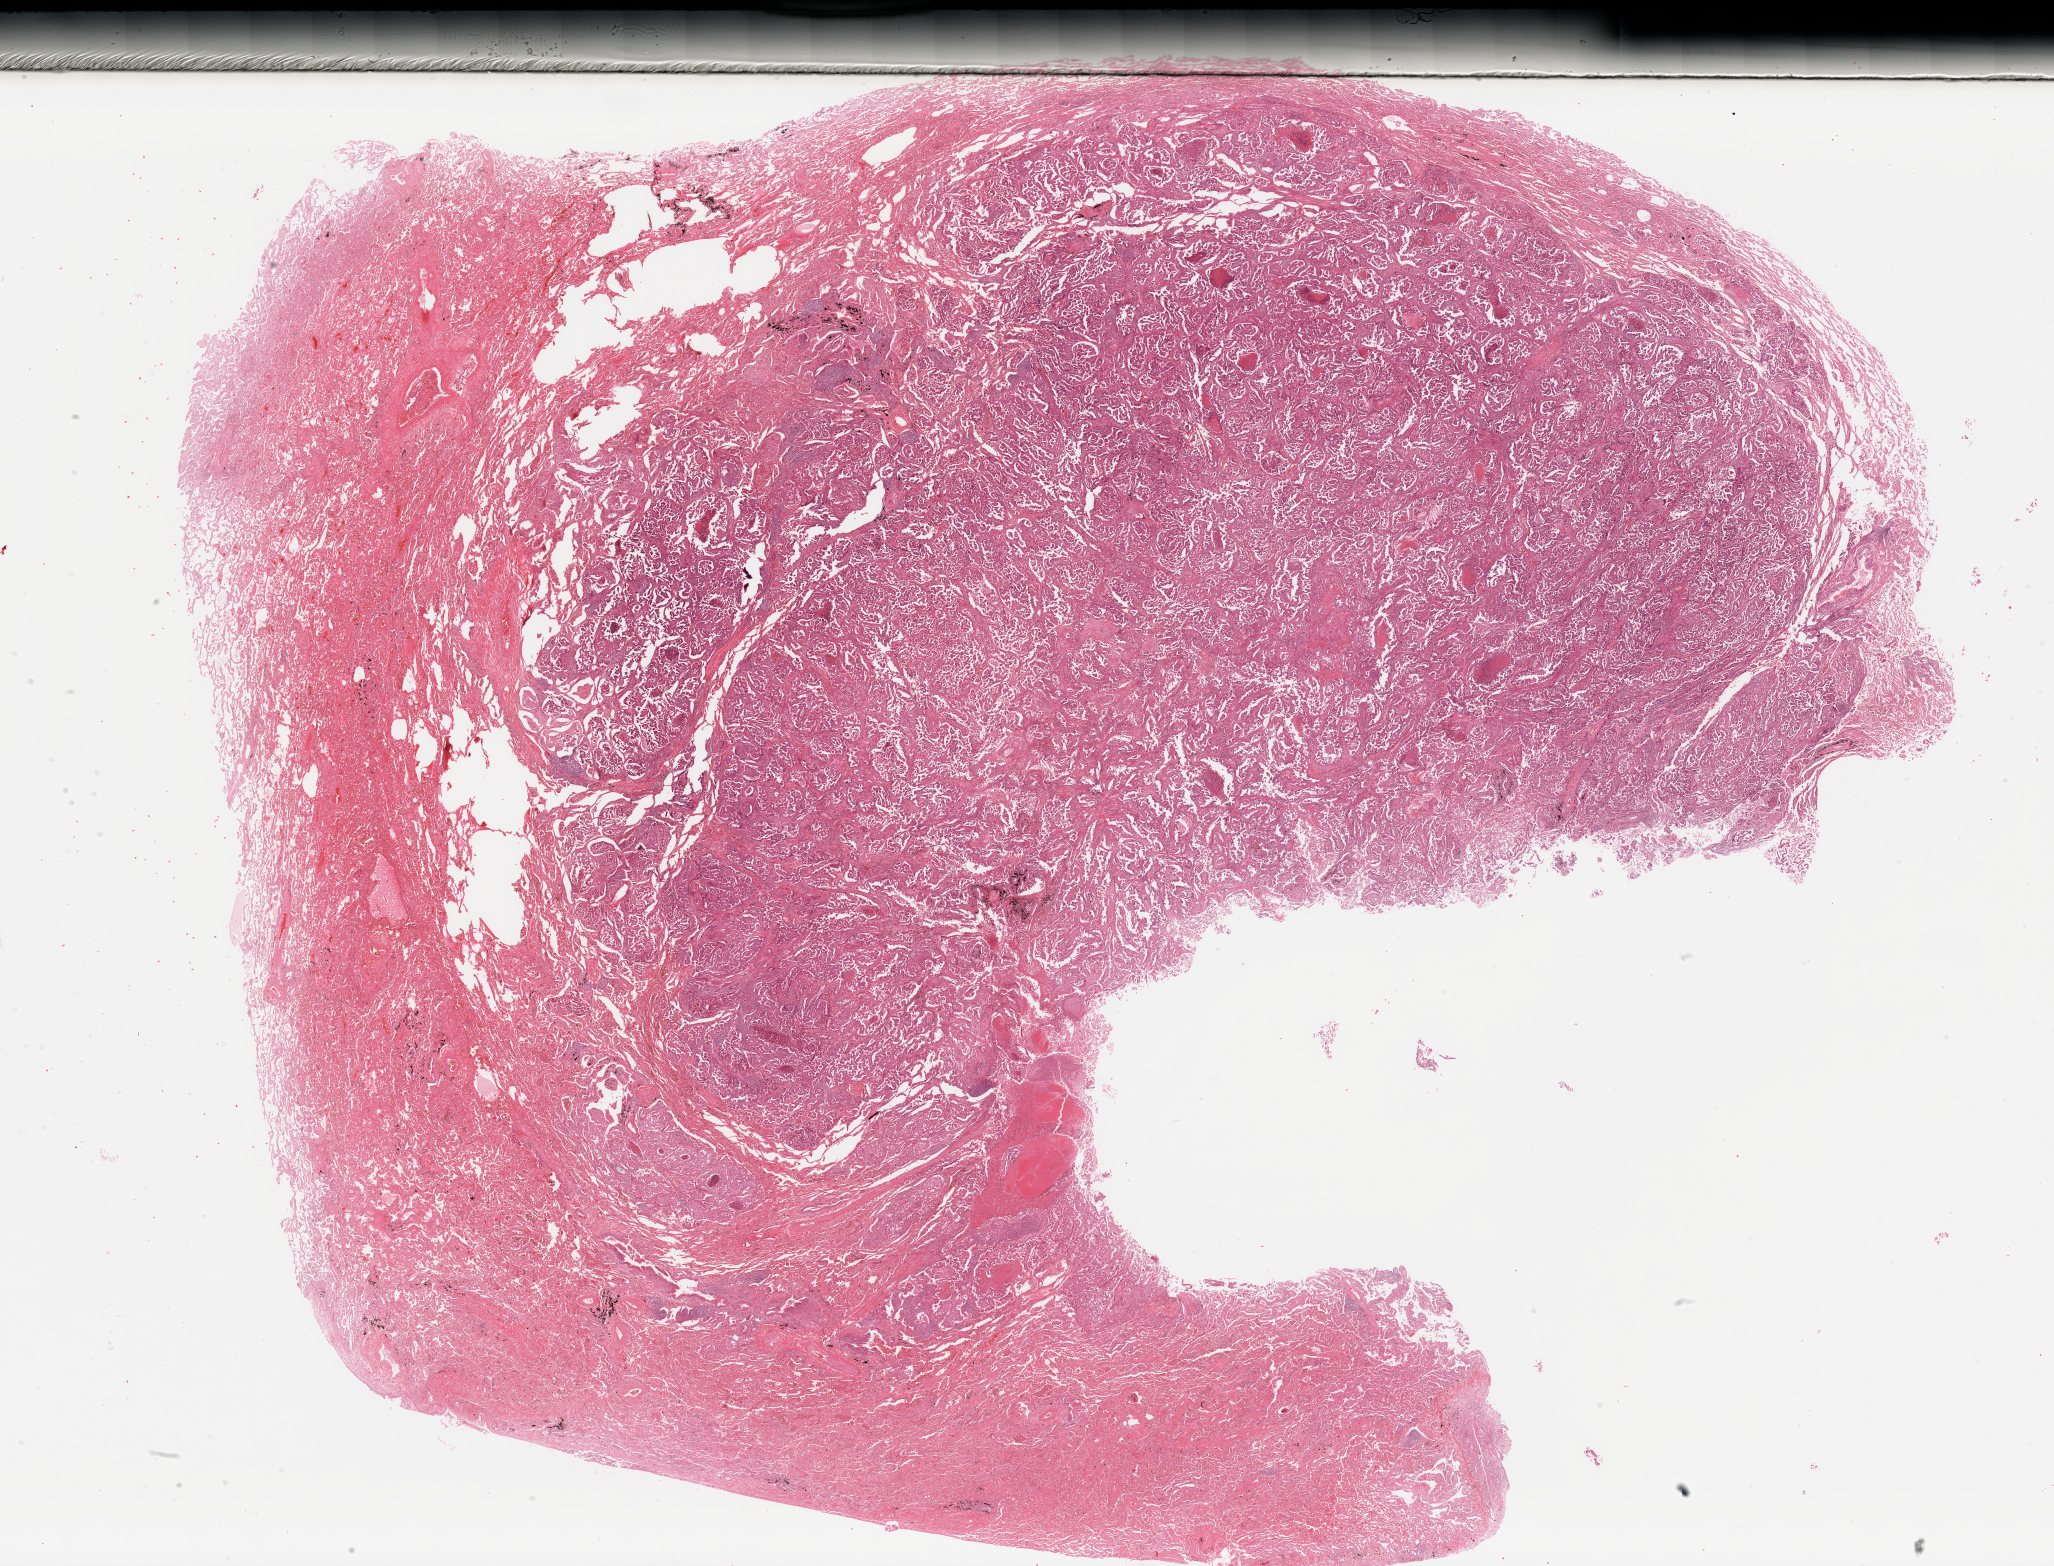
Whole-slide histology image, Hematoxylin and eosin (H&E) stained — whole scanned area (about 32.5 x 24.8 mm) shown as a low-resolution overview, tumour tissue sample, lung. 59-year-old male patient.
Histologic diagnosis: Adenocarcinoma, NOS.